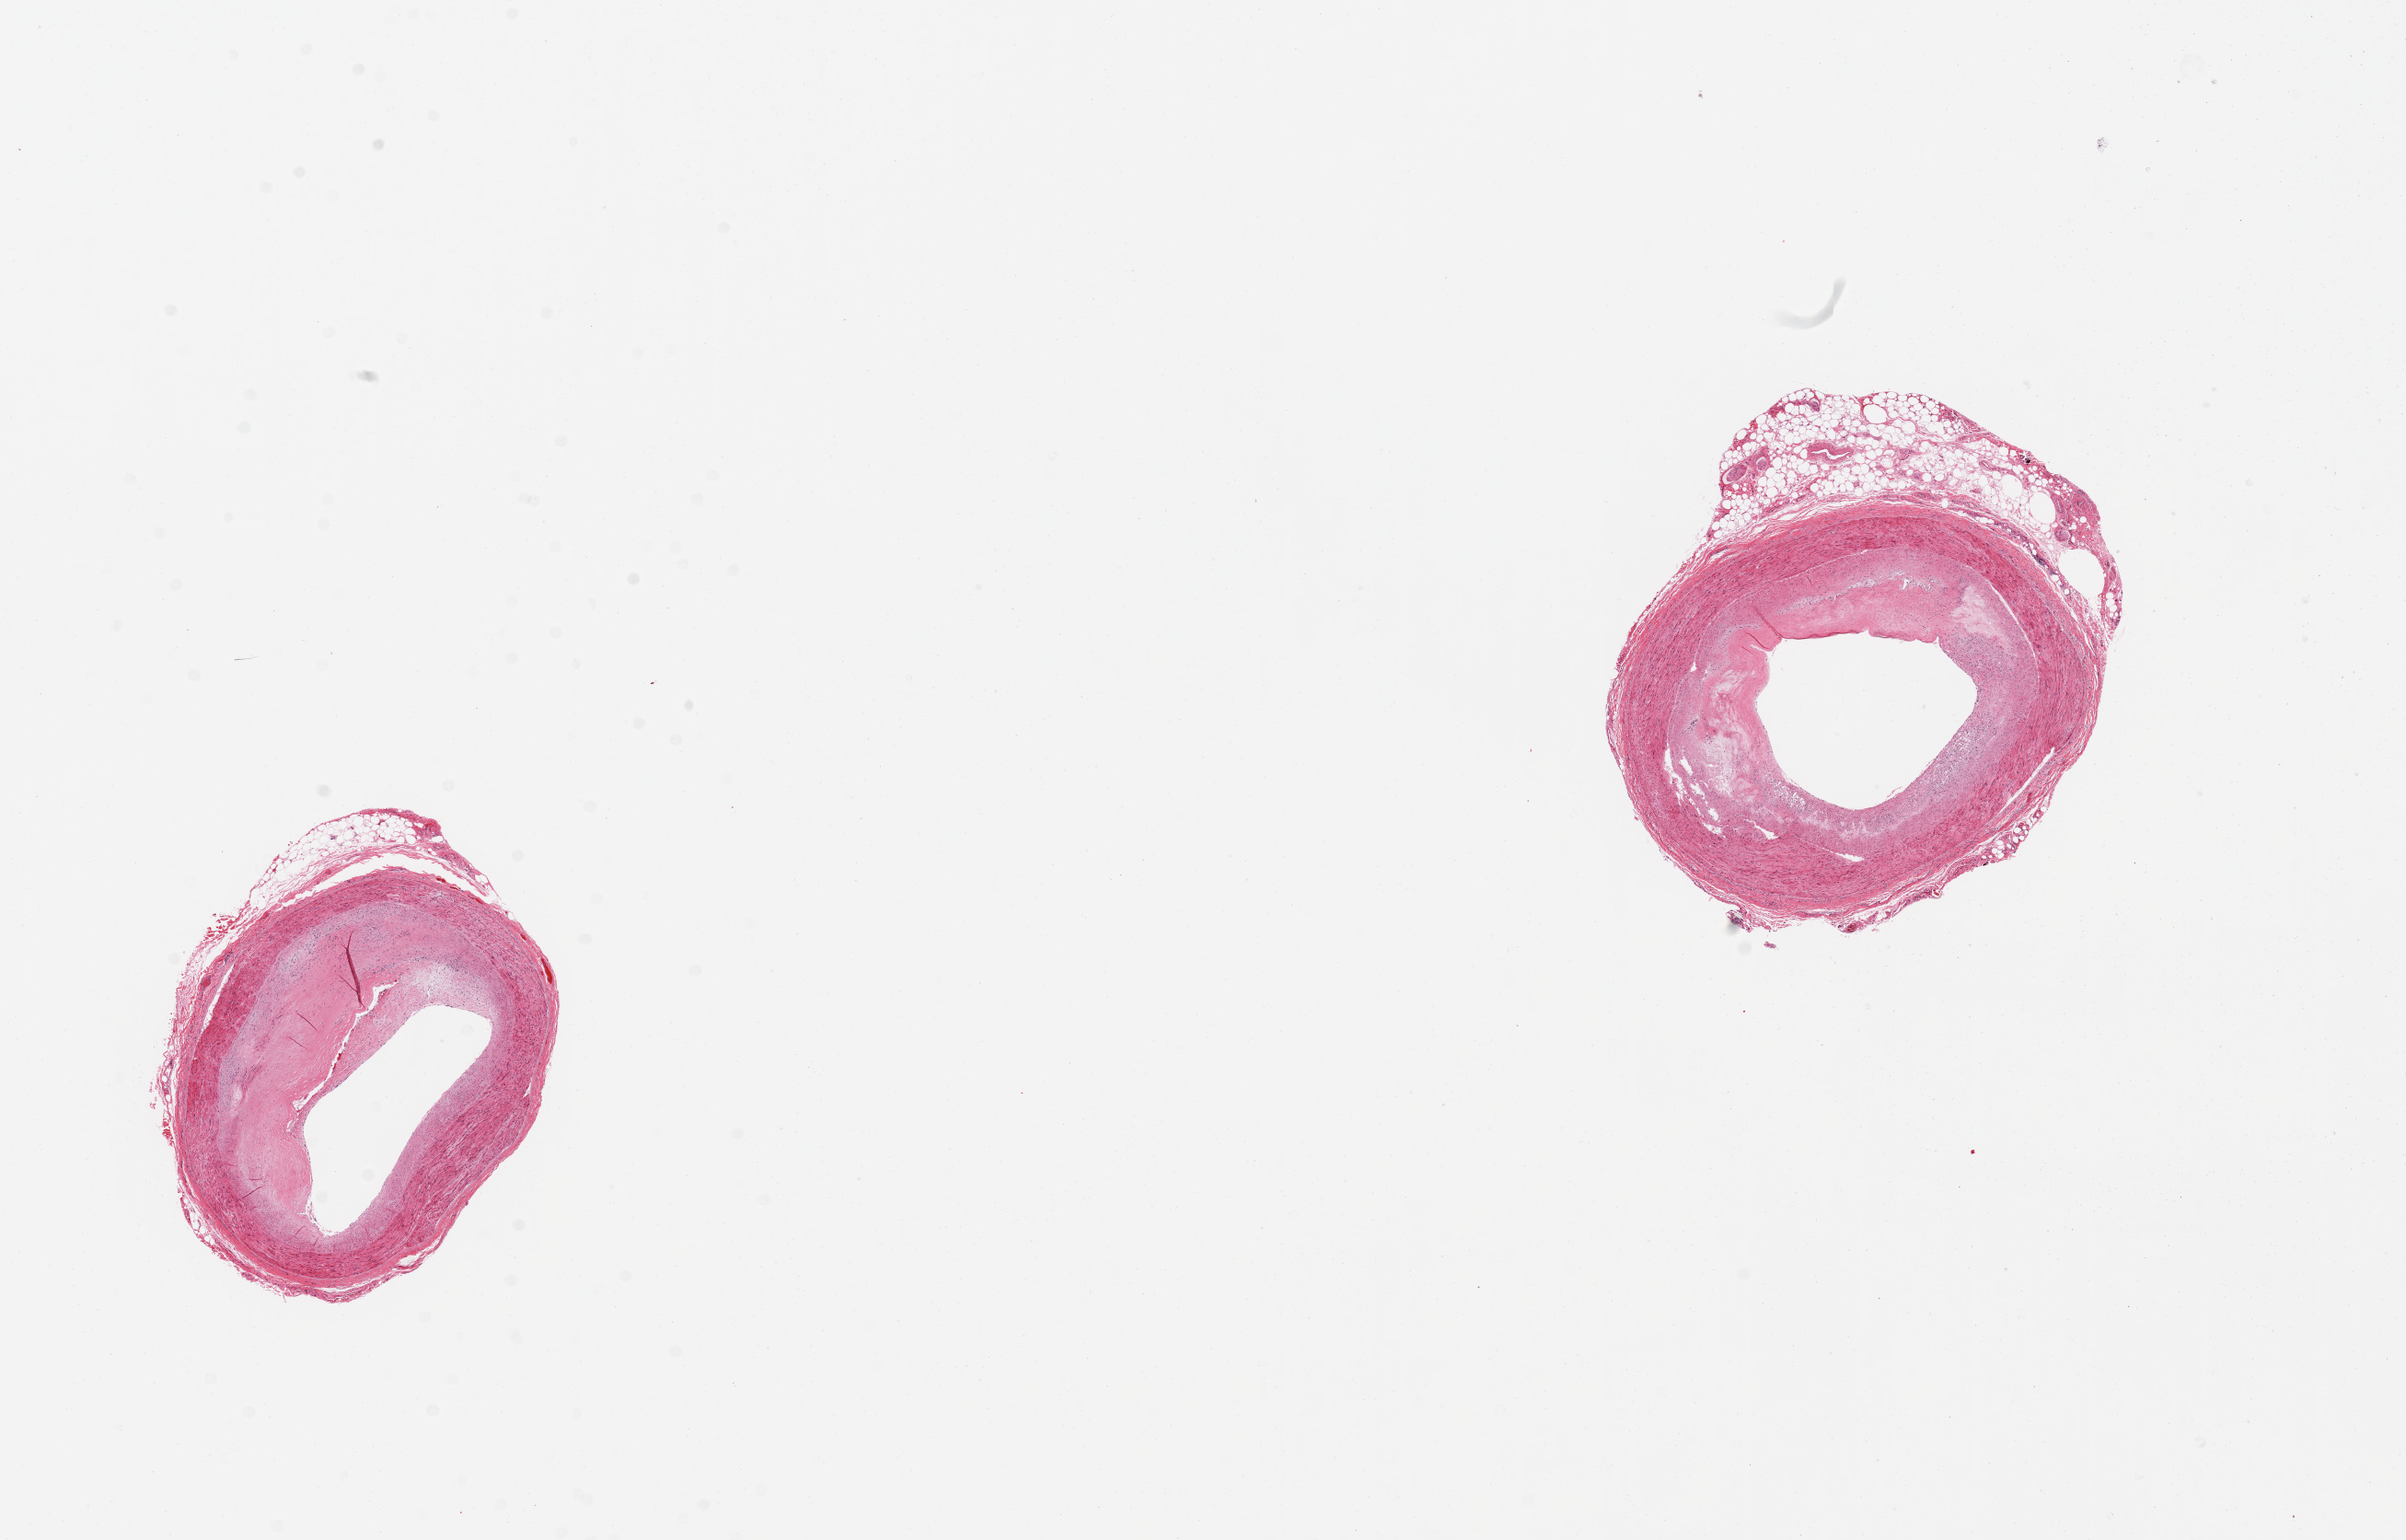
Digitized haematoxylin and eosin-stained section — a low-resolution overview of the entire scanned area, about 20.7 x 13.2 mm (slide scanned at 20x); PAXgene-fixed, paraffin-embedded tissue; sampled site (target tissue): coronary artery; donor tissue sample. Donor sex: male.
* review note (as recorded): 2 pieces, atherosclerosis with narrowing of the lumen by 50%, attached portion of fat up to 3.2x1mm